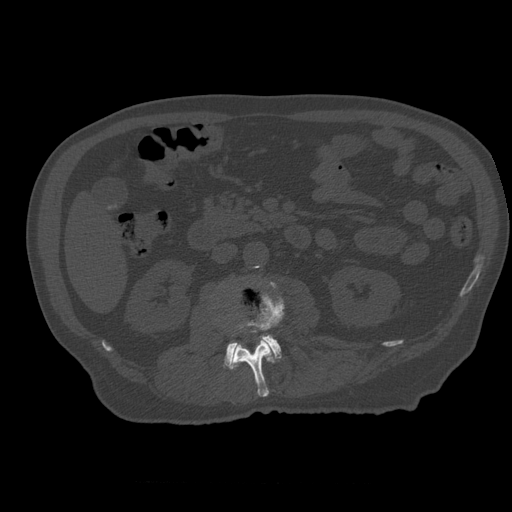
CT including the spine, one axial slice. Position 204 of 399 along the scan axis. Reconstruction kernel STANDARD. Bone window (W 1800 / L 400 HU). 1.25 mm slice thickness. 512 × 512 image matrix, field of view 407 × 407 mm. Patient age 73 years. Case-level facts recorded for this patient, not image findings: primary cancer: prostate.
Structures marked on this image (semi-automatic segmentation, software-assisted and operator-edited):
- L2 vertebra: box from (x=230, y=286) to (x=285, y=397) px
- L3 vertebra: (x=224, y=283)–(x=283, y=369)